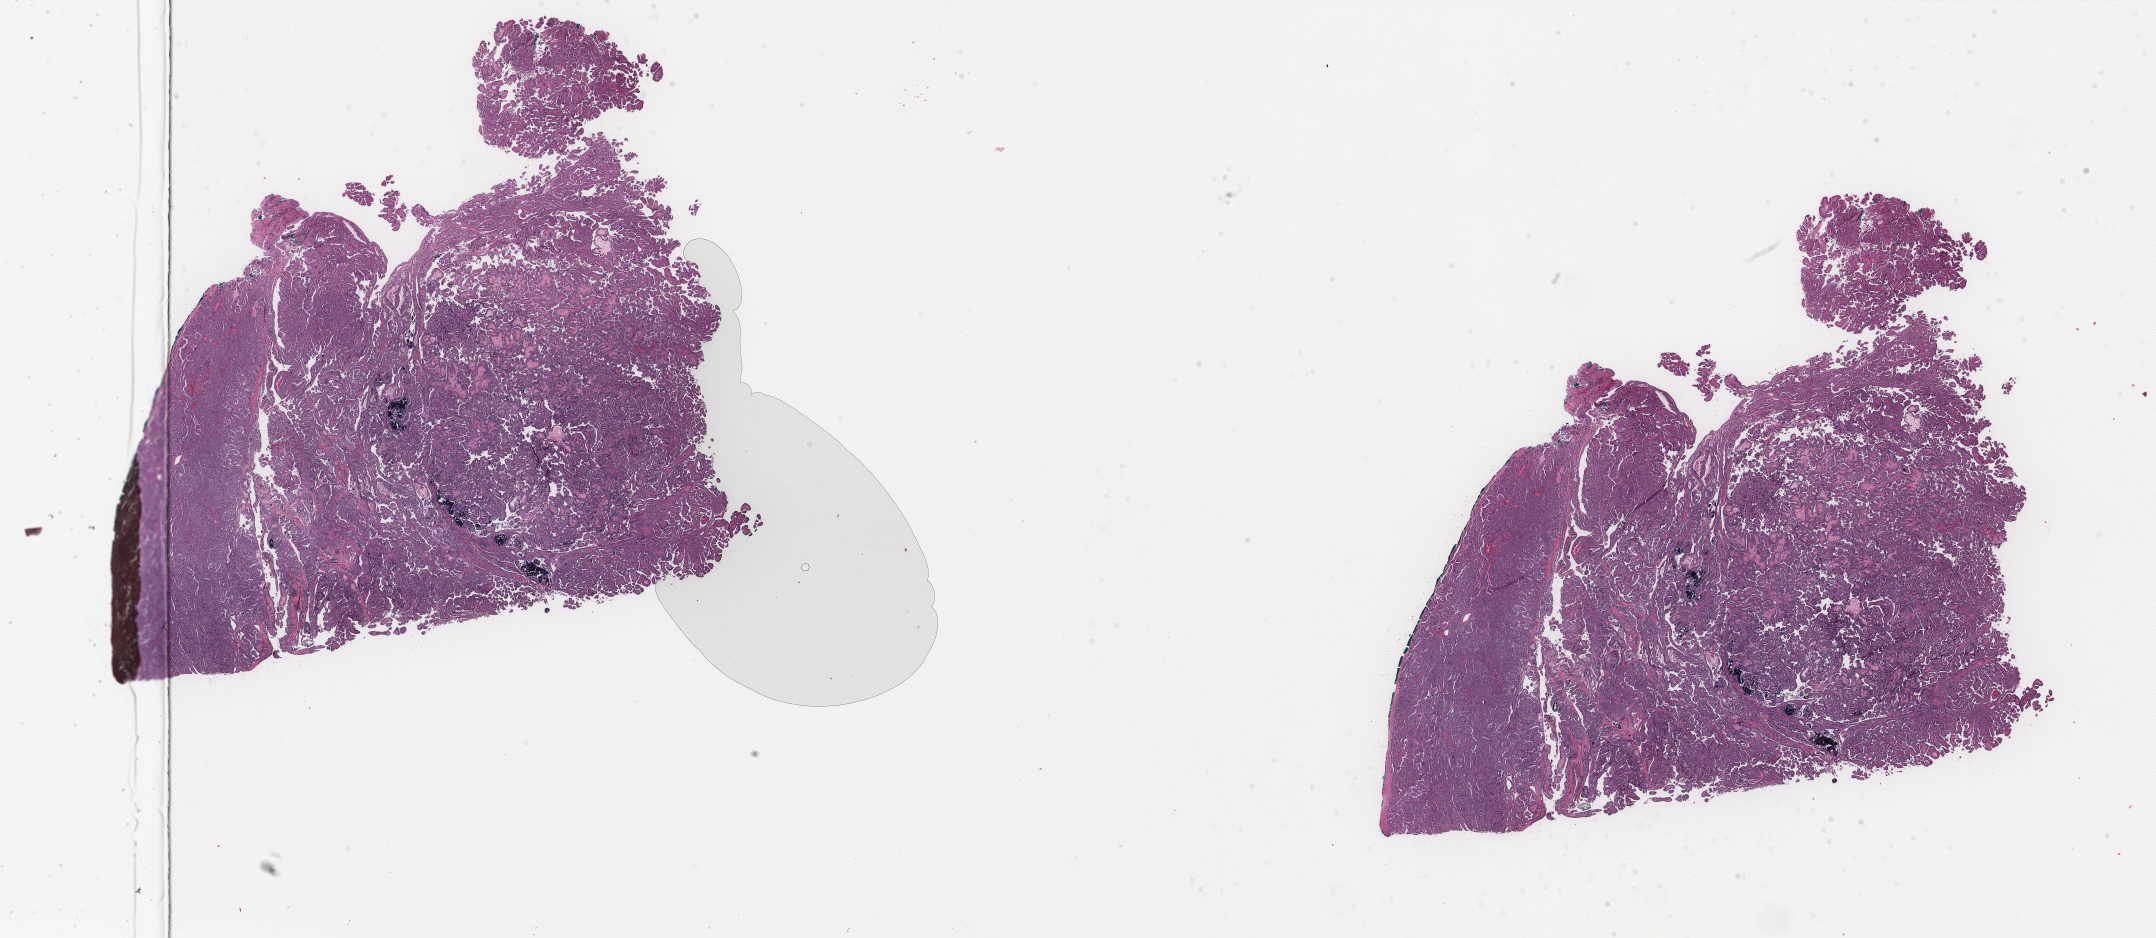
H&E whole-slide image — a low-resolution overview of the entire scanned area, about 34.1 x 14.8 mm, FFPE section, primary tumour sample from the thyroid. Female, age 58 years at initial diagnosis.
Laterality: right. Lymph nodes positive (case pathology): 0 of 4 examined. Histologic diagnosis: Papillary adenocarcinoma, NOS (thyroid gland). AJCC pathologic stage: III (7th edition).